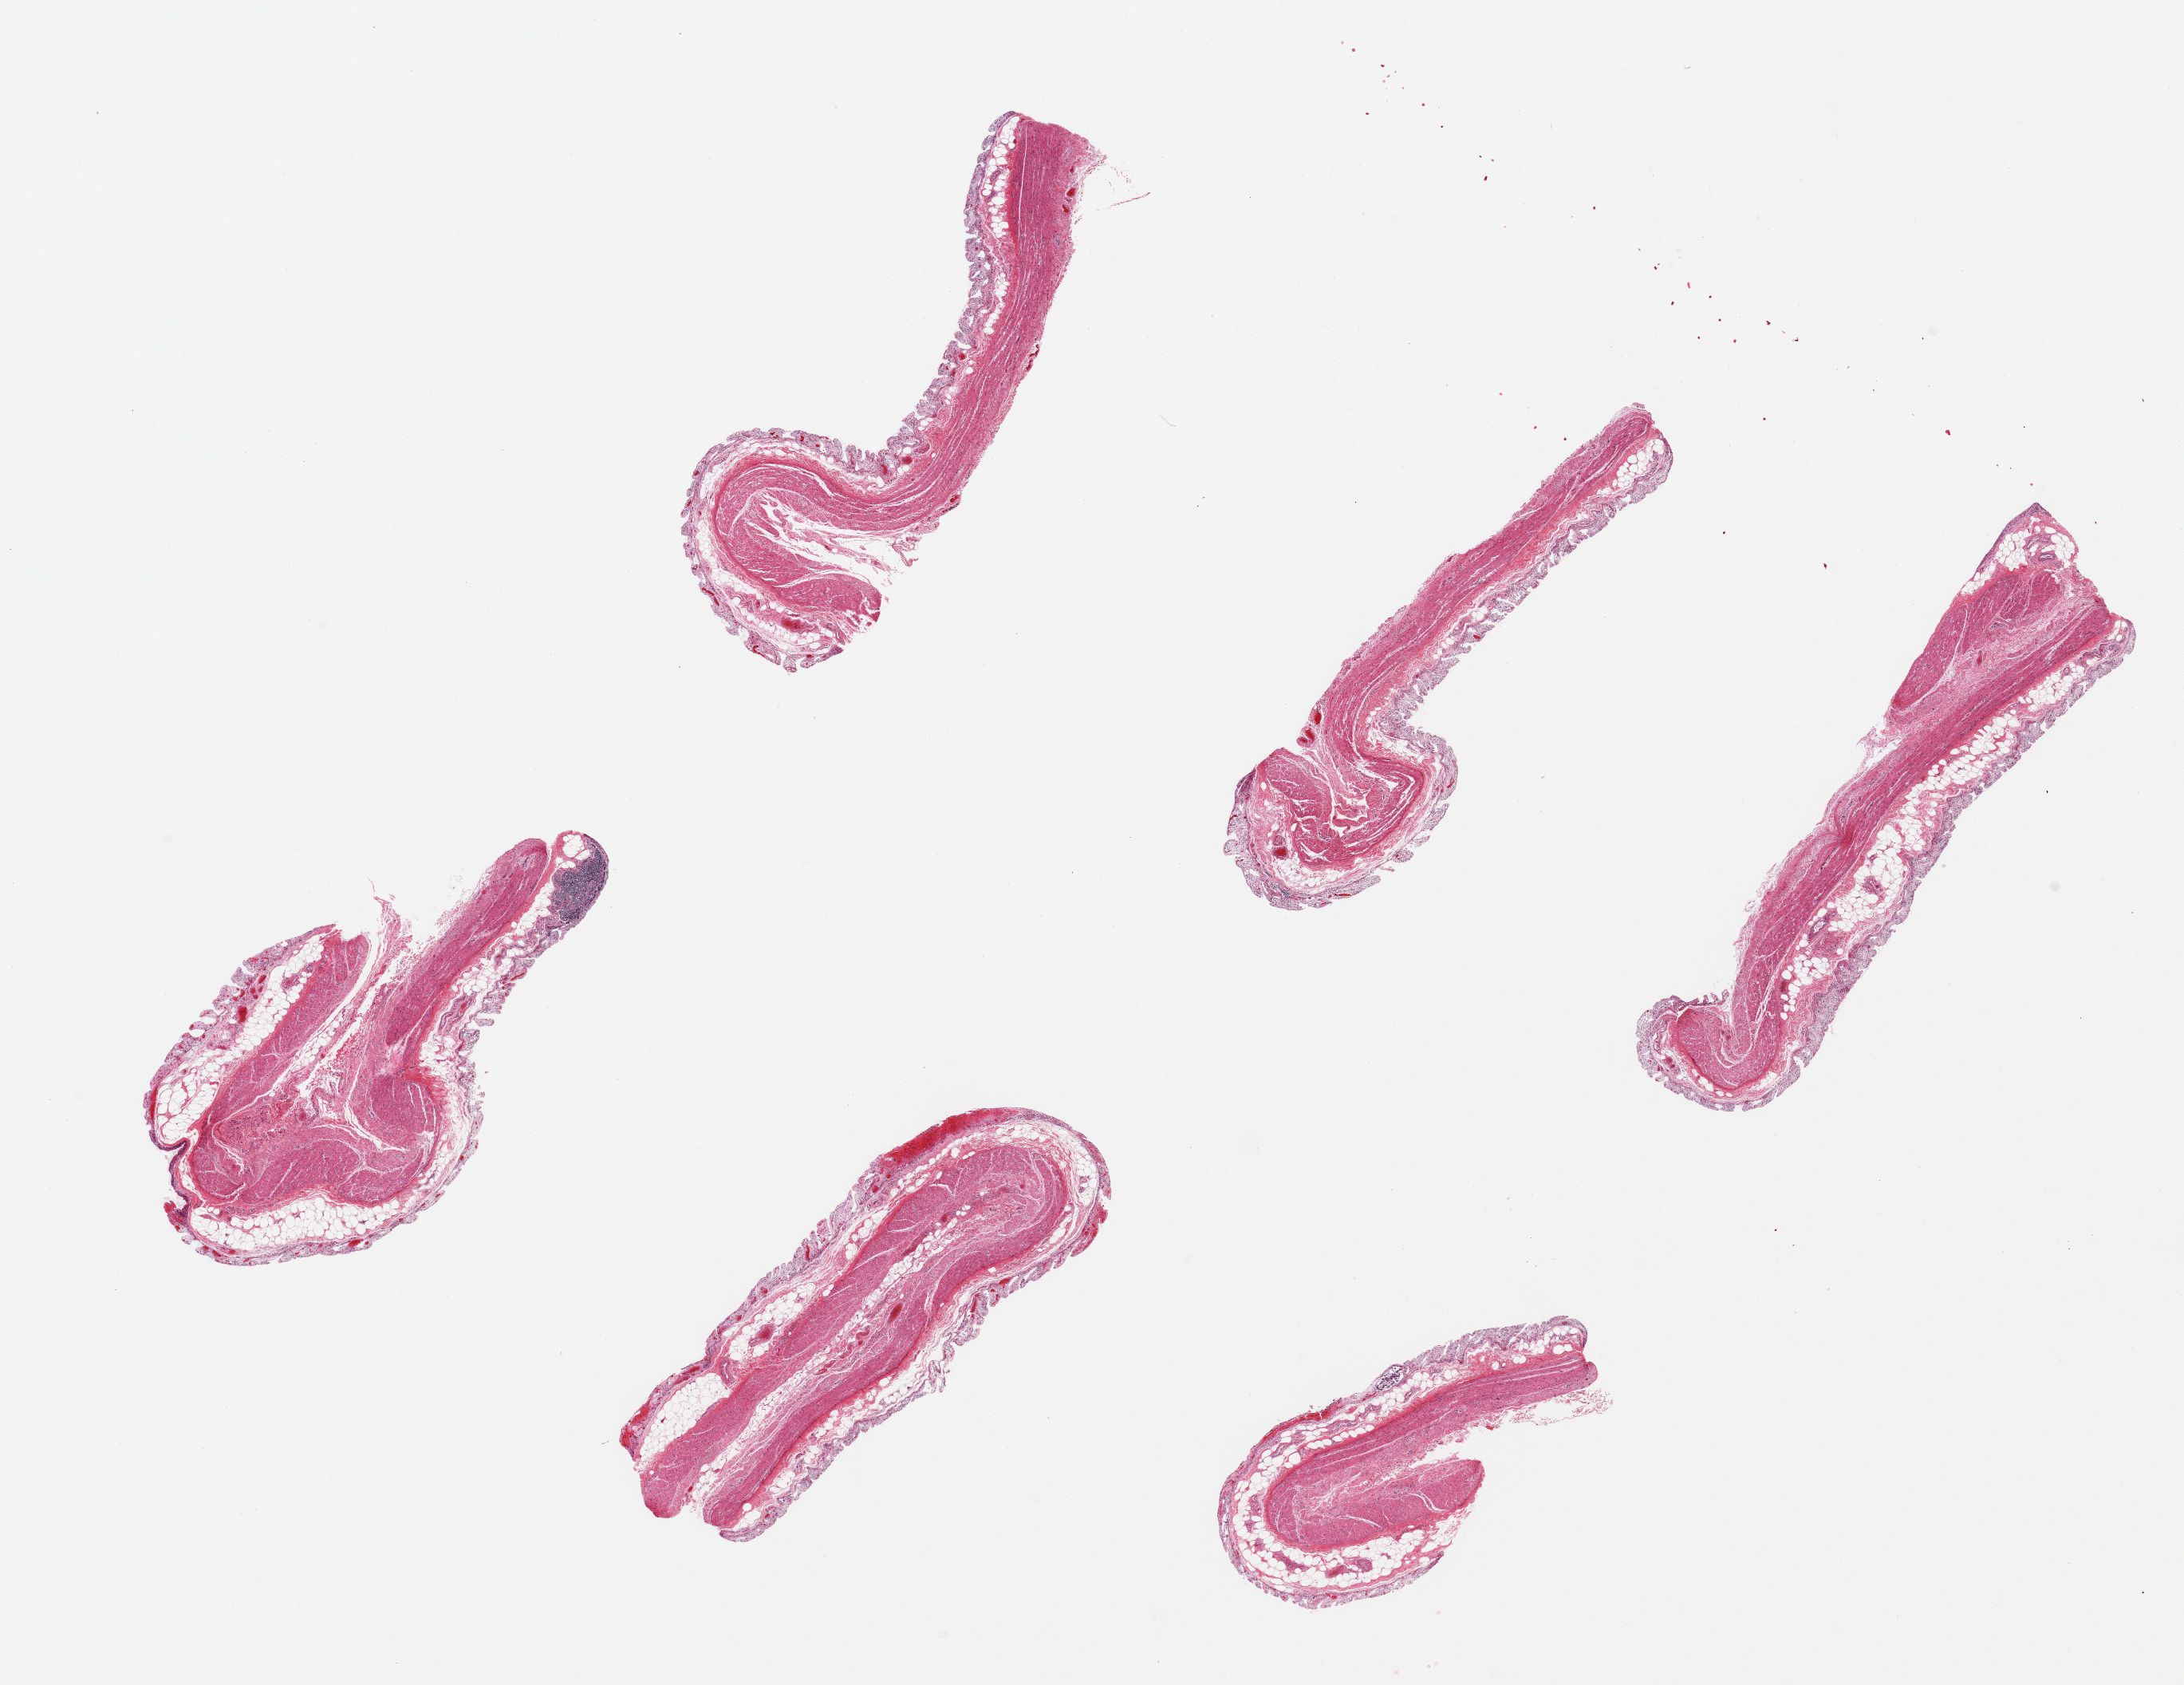
Haematoxylin and eosin whole-slide image, shown as a low-resolution overview of the whole scanned area (about 21.7 x 16.7 mm). PAXgene-fixed, paraffin-embedded tissue. Sampled site (target tissue): transverse colon. Tissue donor sample.
Review note (as recorded): 6 pieces ~8x3mm, mucosa completely auotlyzed.